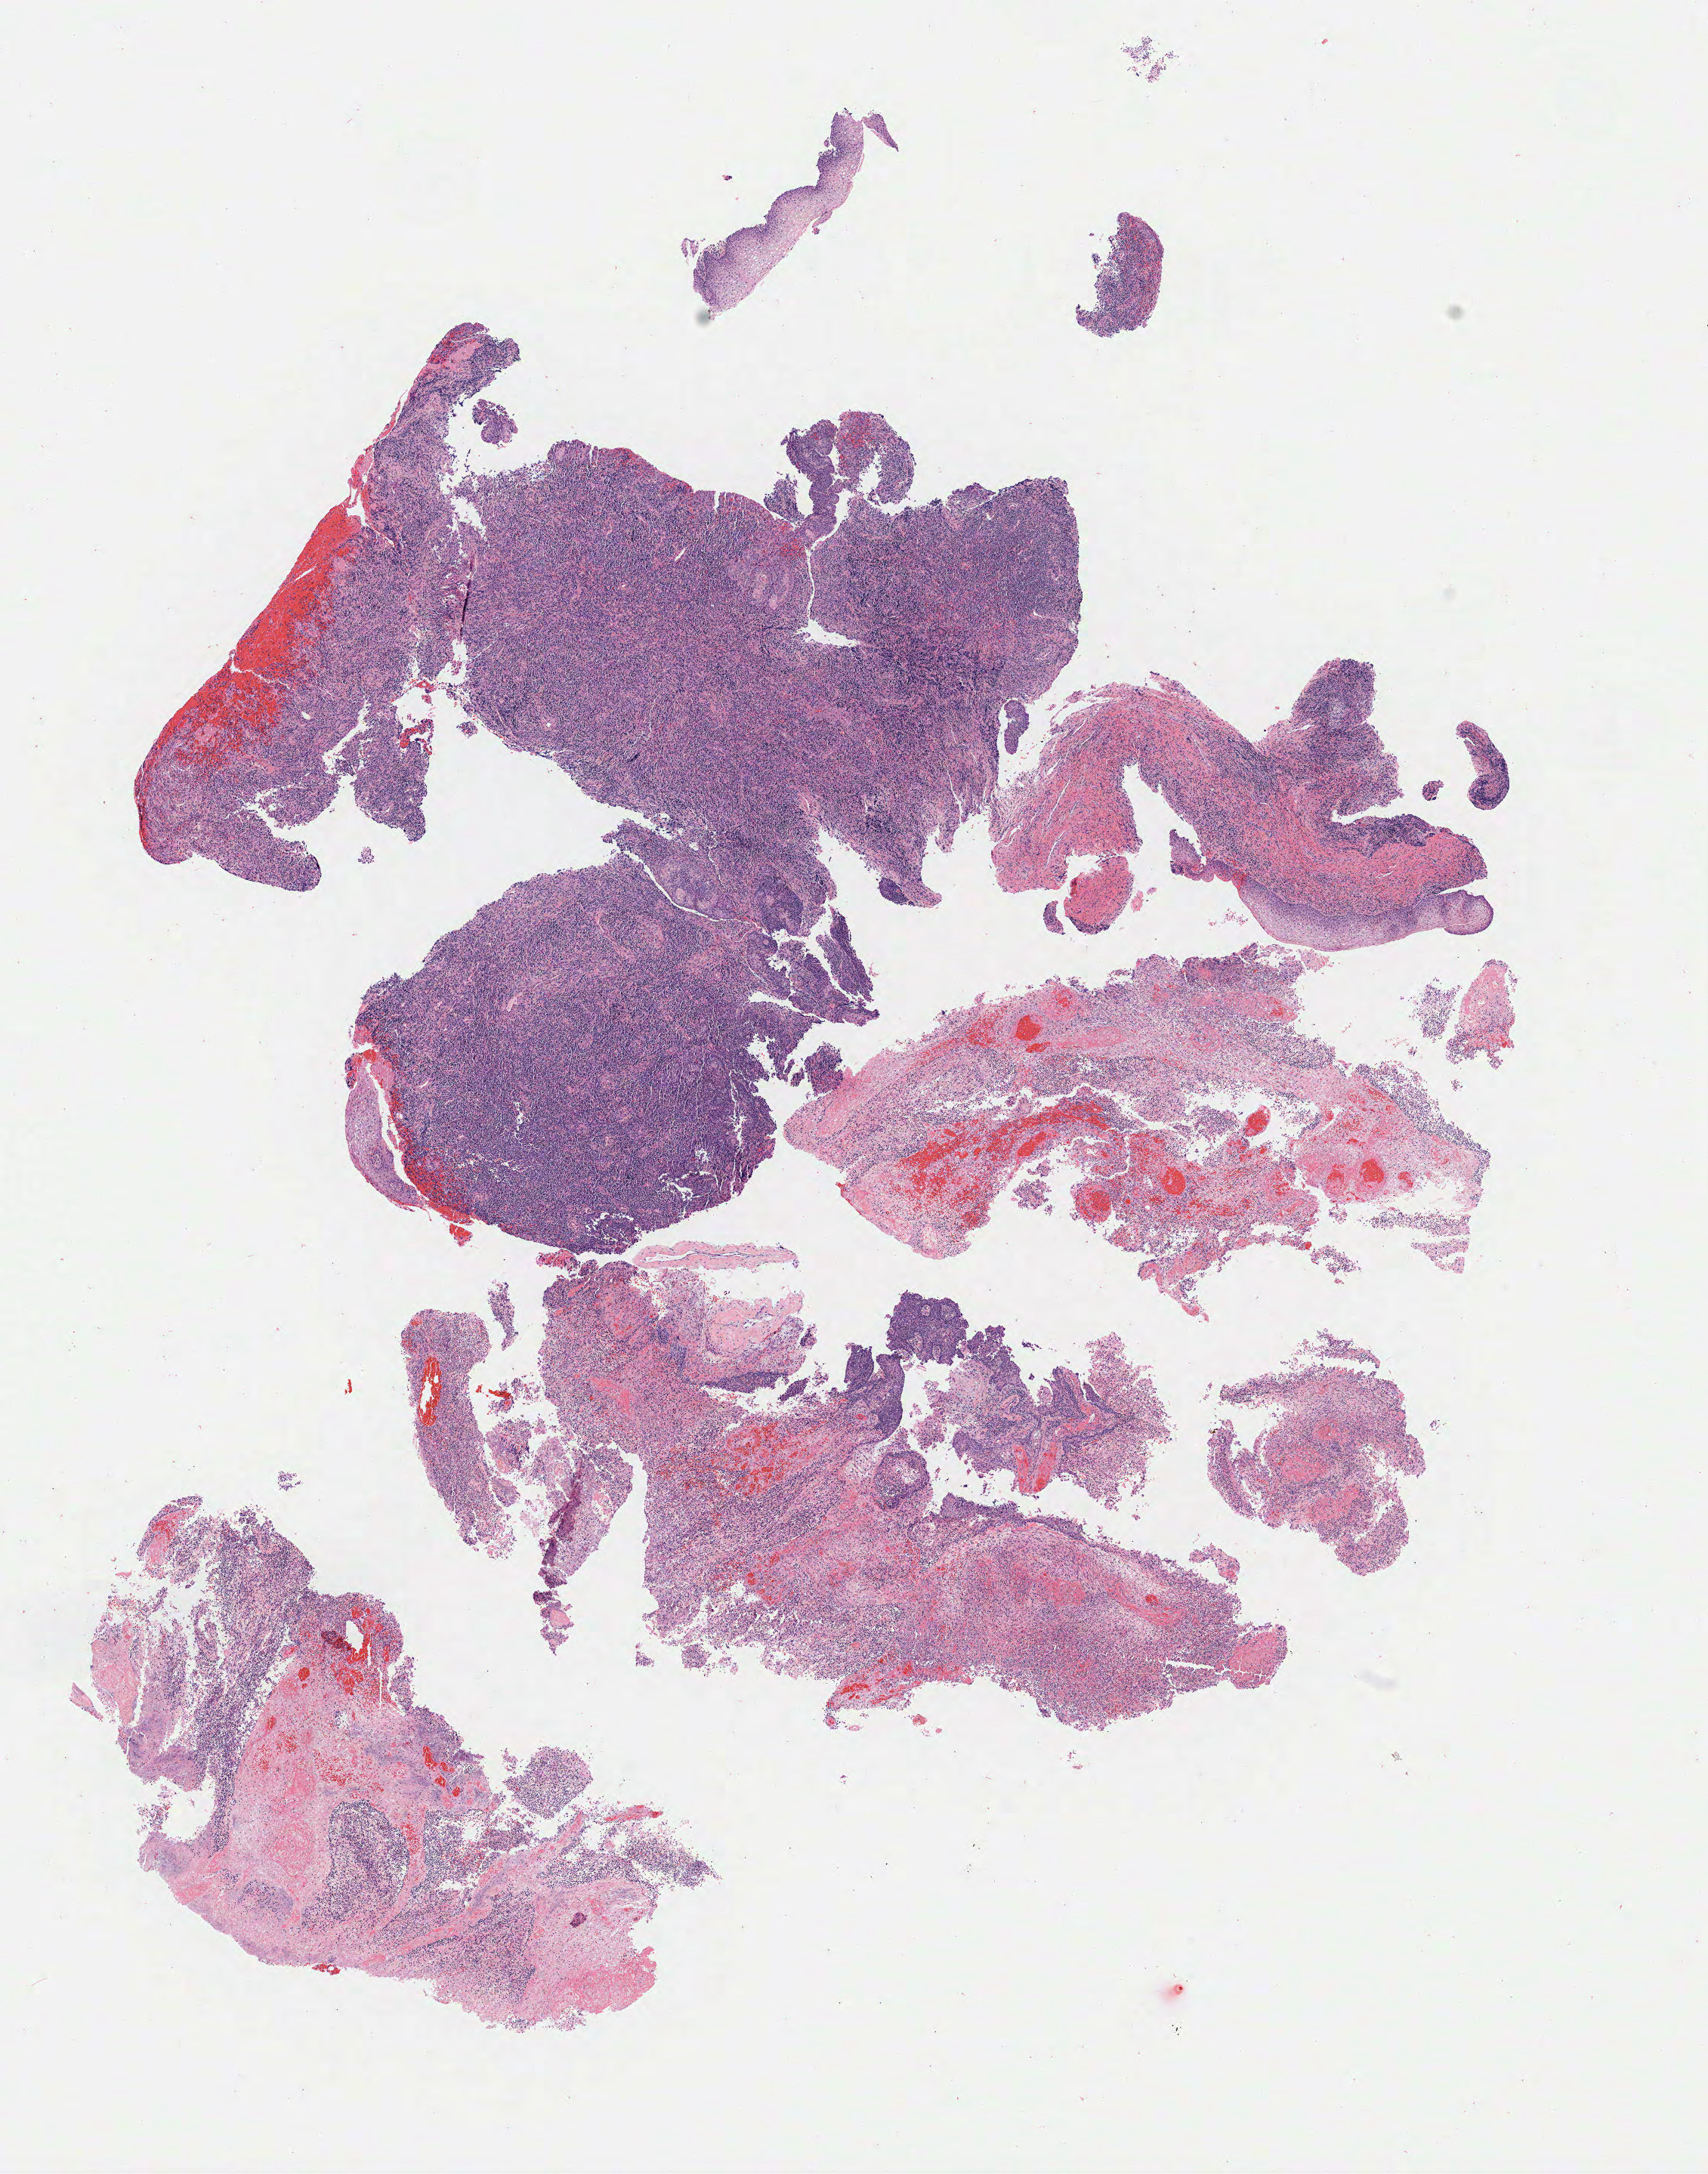
Whole-slide image, hematoxylin and eosin (H&E) stain — whole scanned area (about 9.0 x 11.4 mm) shown as a low-resolution overview, specimen: tumor tissue, site: cervix. Patient female; age 61 years.
Diagnosis: Squamous cell carcinoma, large cell, nonkeratinizing, NOS.